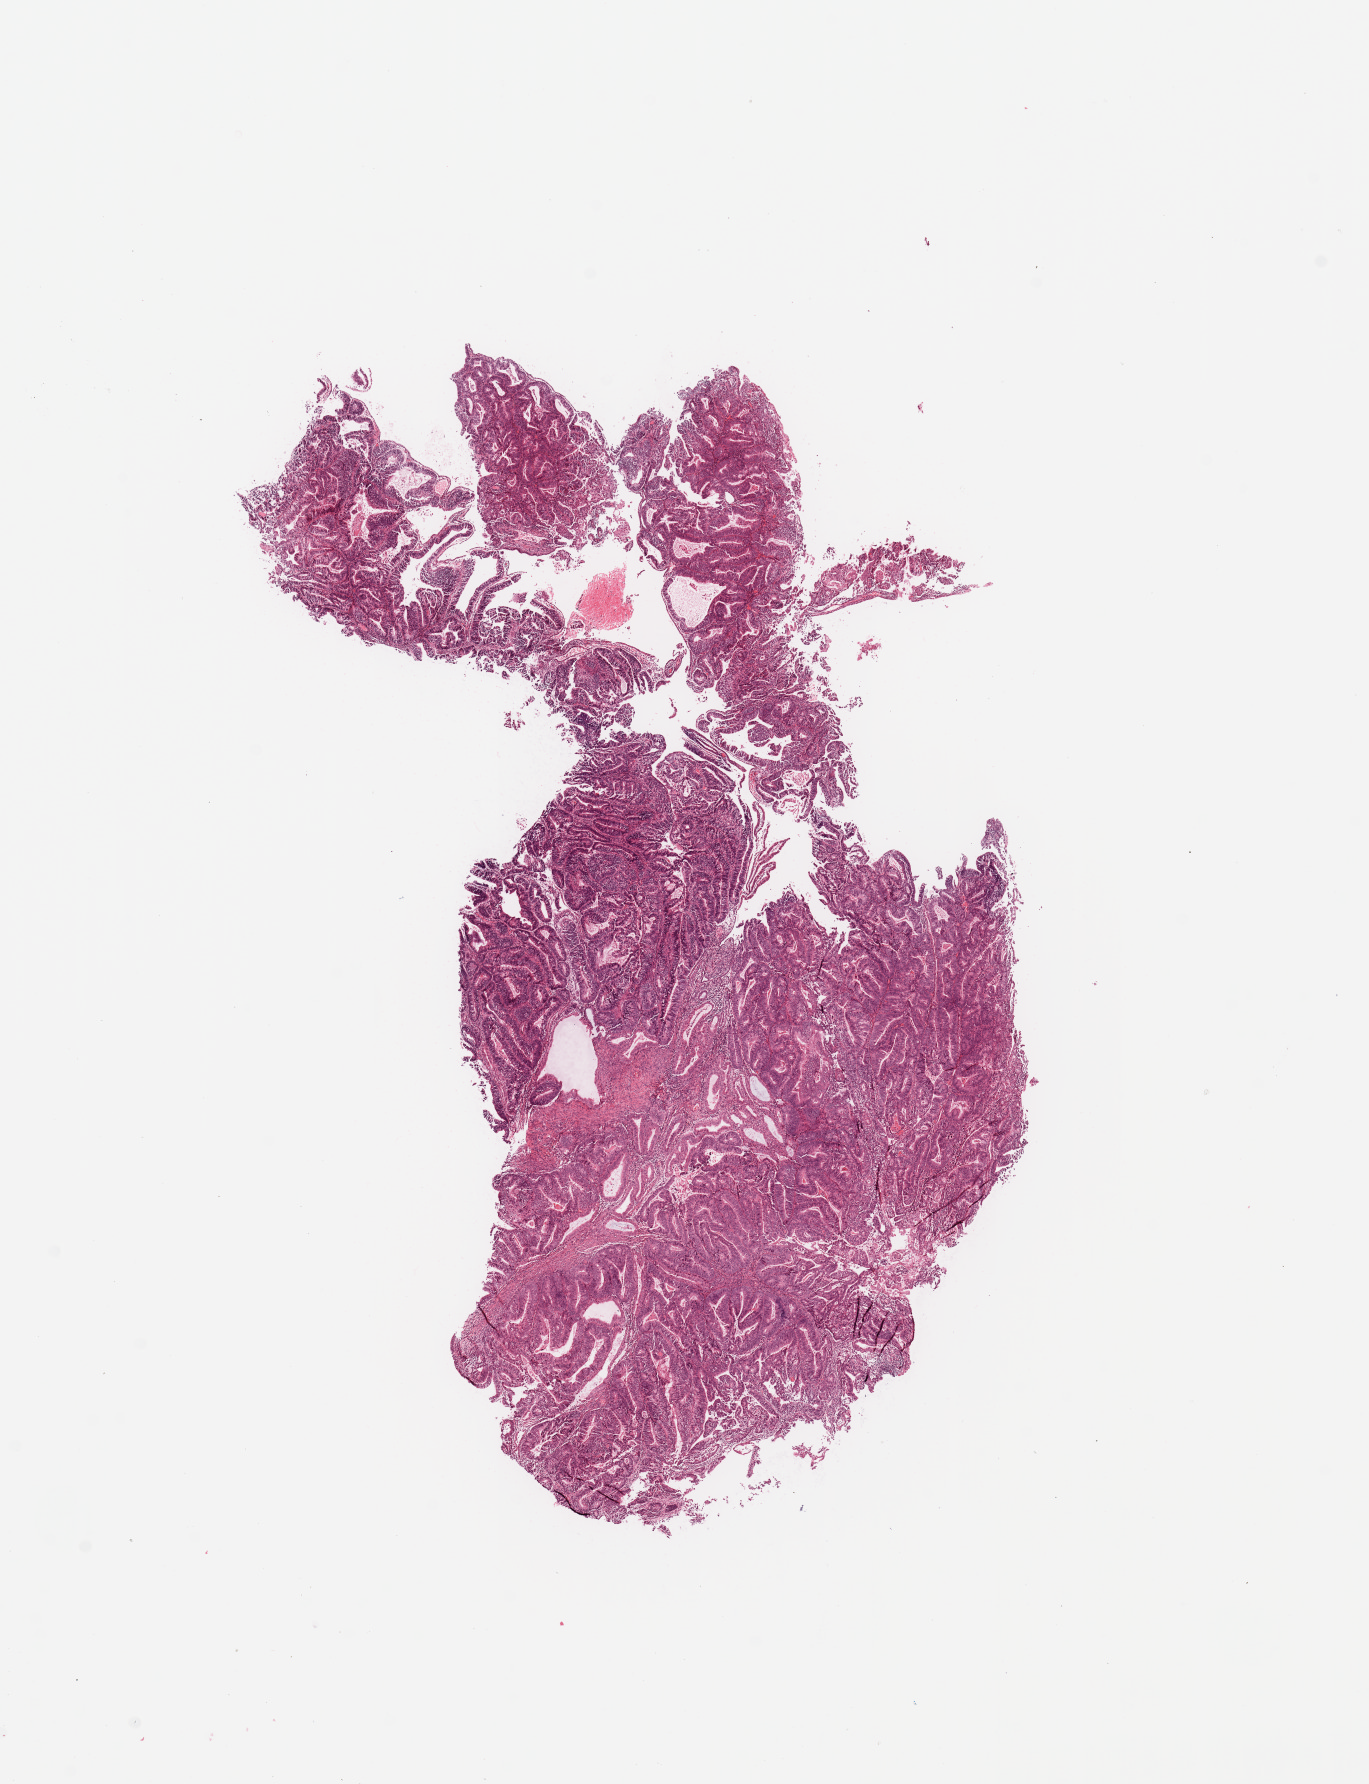
Whole-slide histology image, H&E-stained, whole scanned area (about 10.8 x 14.1 mm) shown as a low-resolution overview, tumour tissue sample, uterus. Patient: female, age 59 years. Histologic grade: G1 (well differentiated).
- diagnosis: Endometrioid adenocarcinoma, NOS
- AJCC pathologic stage: IA